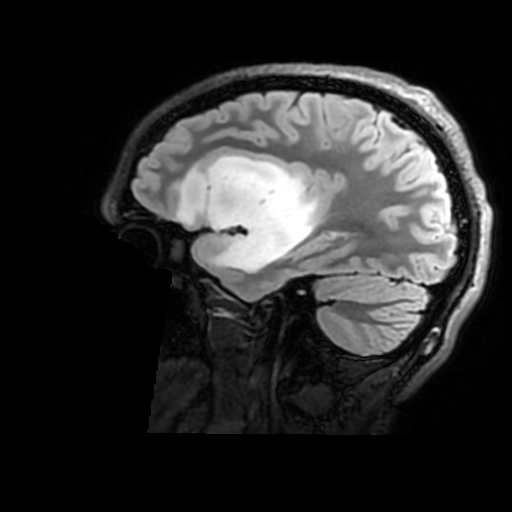
Brain MRI from a brain-tumour surgery series, one sagittal slice. Position 123 of 176 along the scan axis. T2 FLAIR. 1 mm slice thickness. 512 × 512 image matrix. From the clinical record (not read from this slice): histopathology: Astrocytoma; WHO grade: 2; IDH mutation: yes; tumour location: Right Insular.
Structures marked on this image (manually delineated by an expert):
- tumour: bounding box (x1, y1, x2, y2) in pixels: (177, 155, 322, 275)